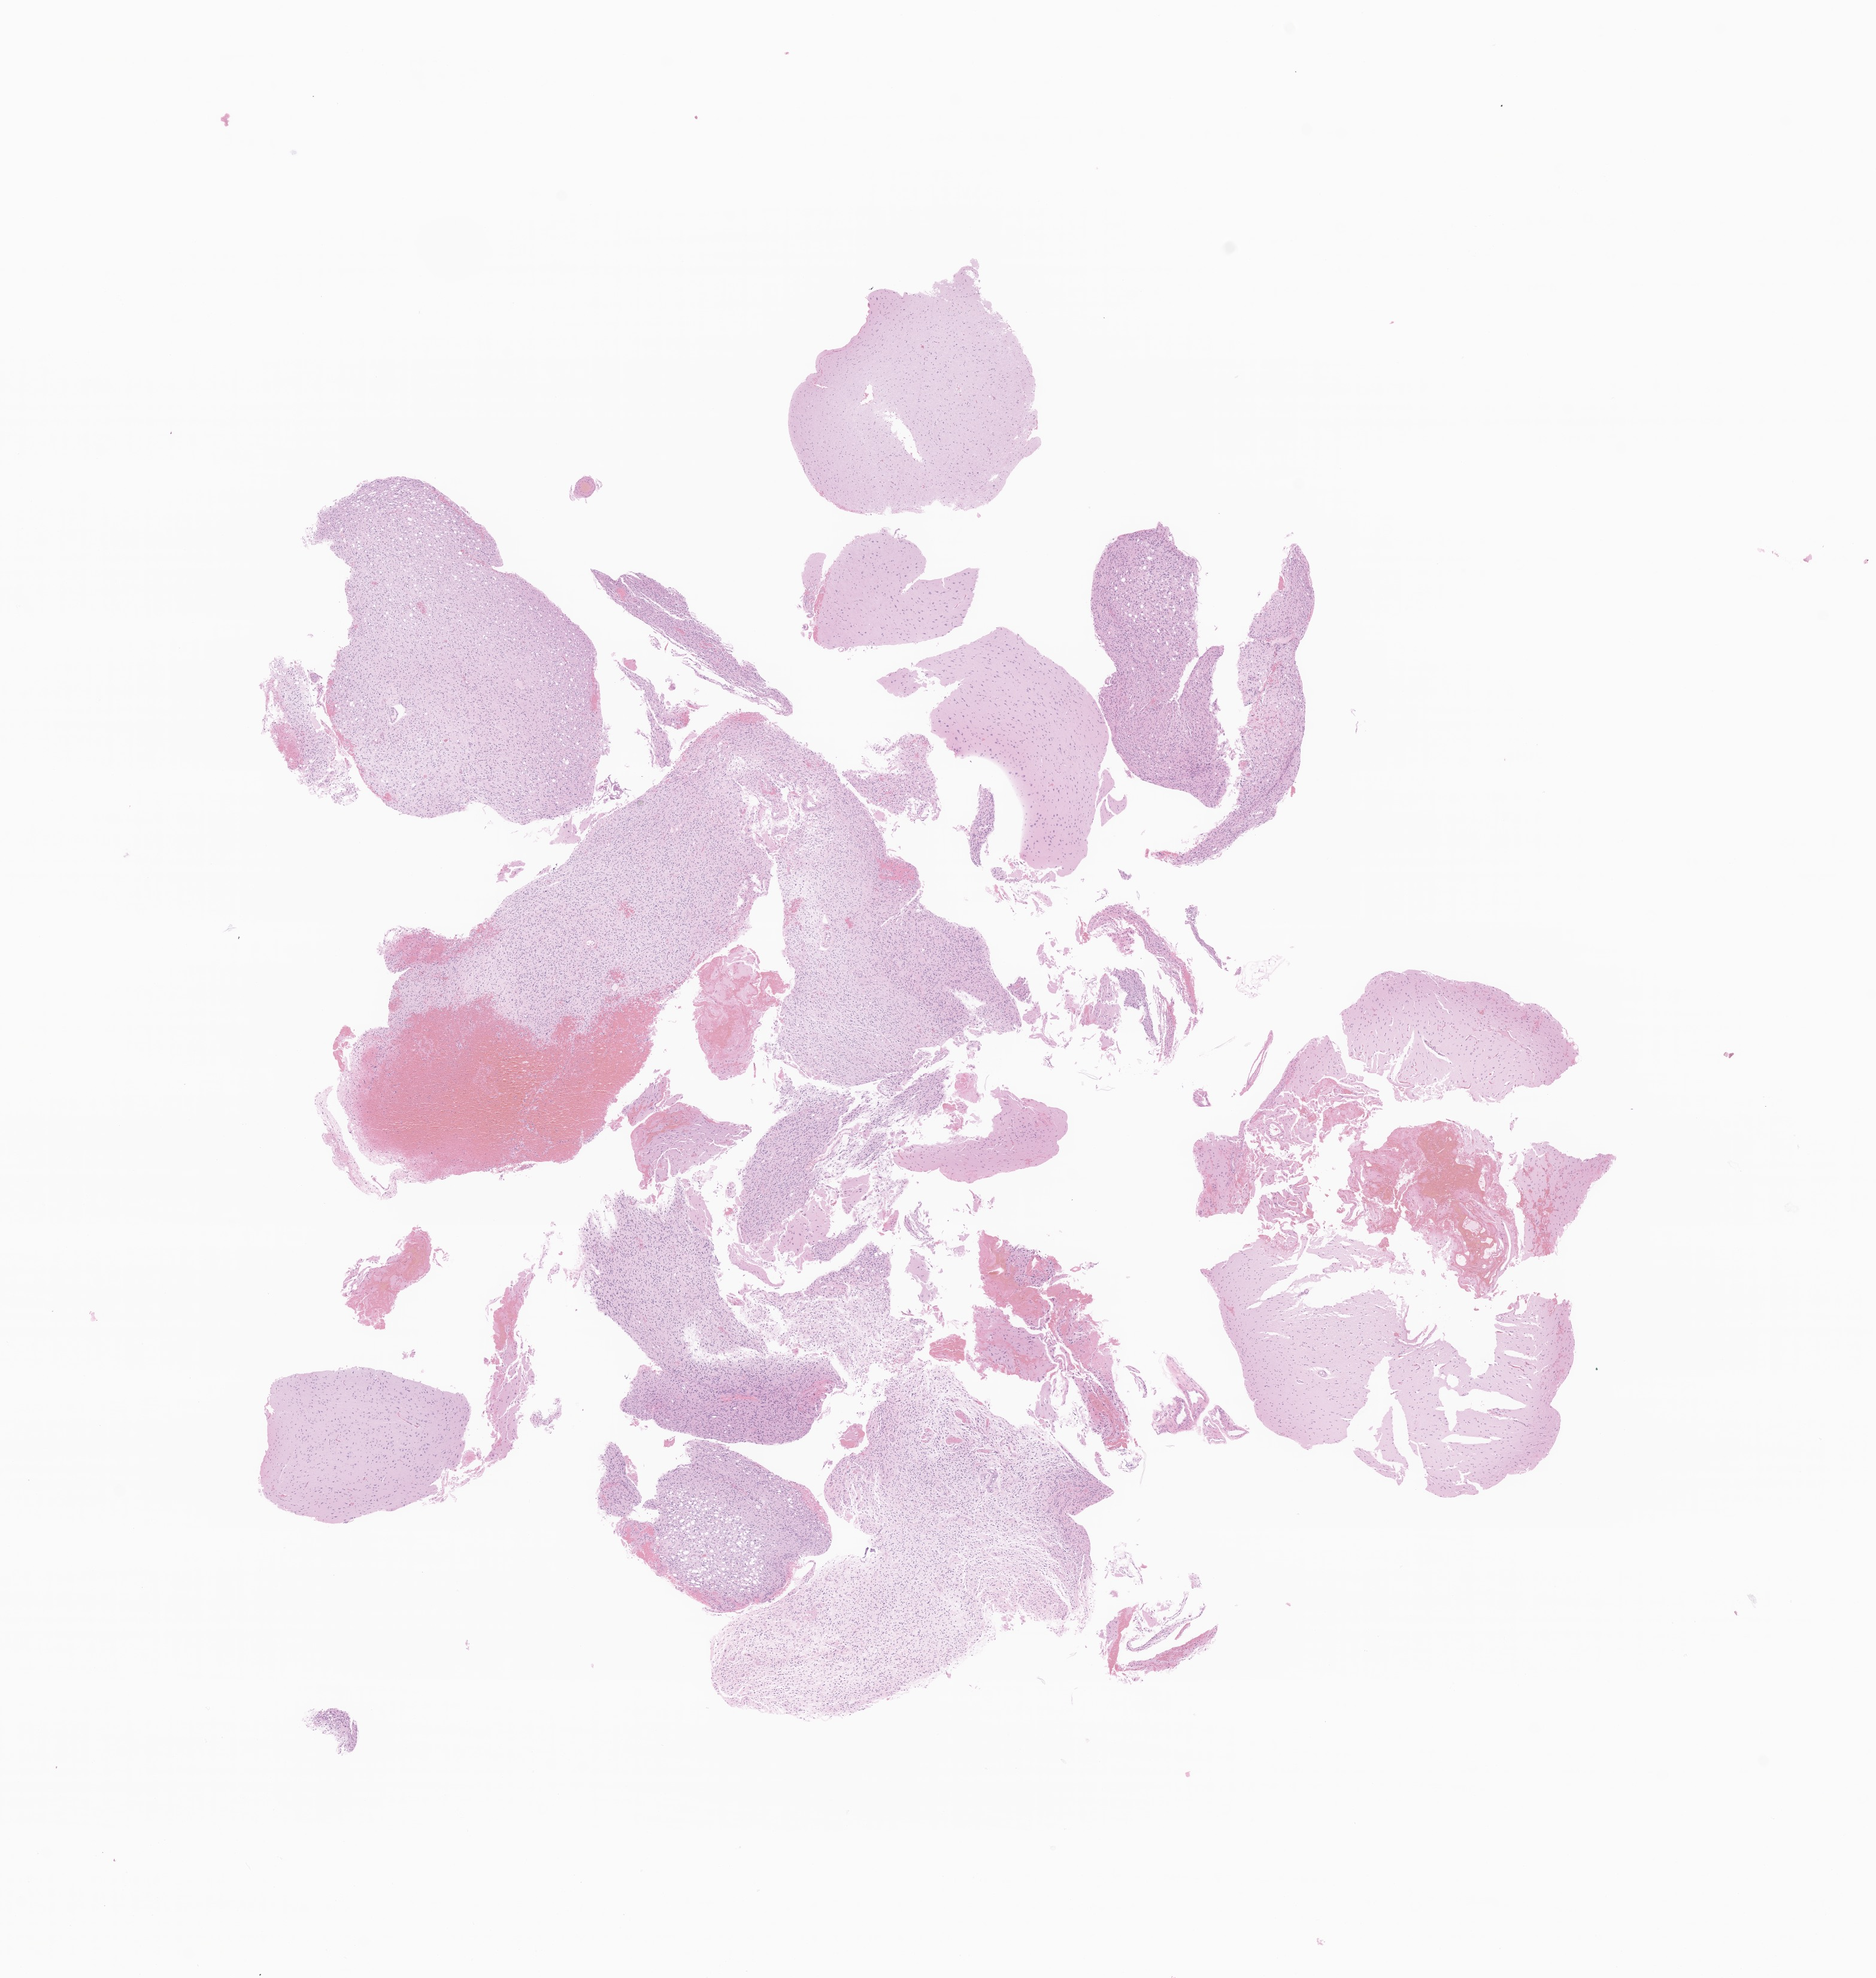
Digitized haematoxylin and eosin-stained section of tumor tissue from the brain, whole scanned area (about 13.2 x 13.9 mm) shown as a low-resolution overview. FFPE section. Female patient, age 169 months (14 years 1 month).
Diagnosis: Glioma, malignant.